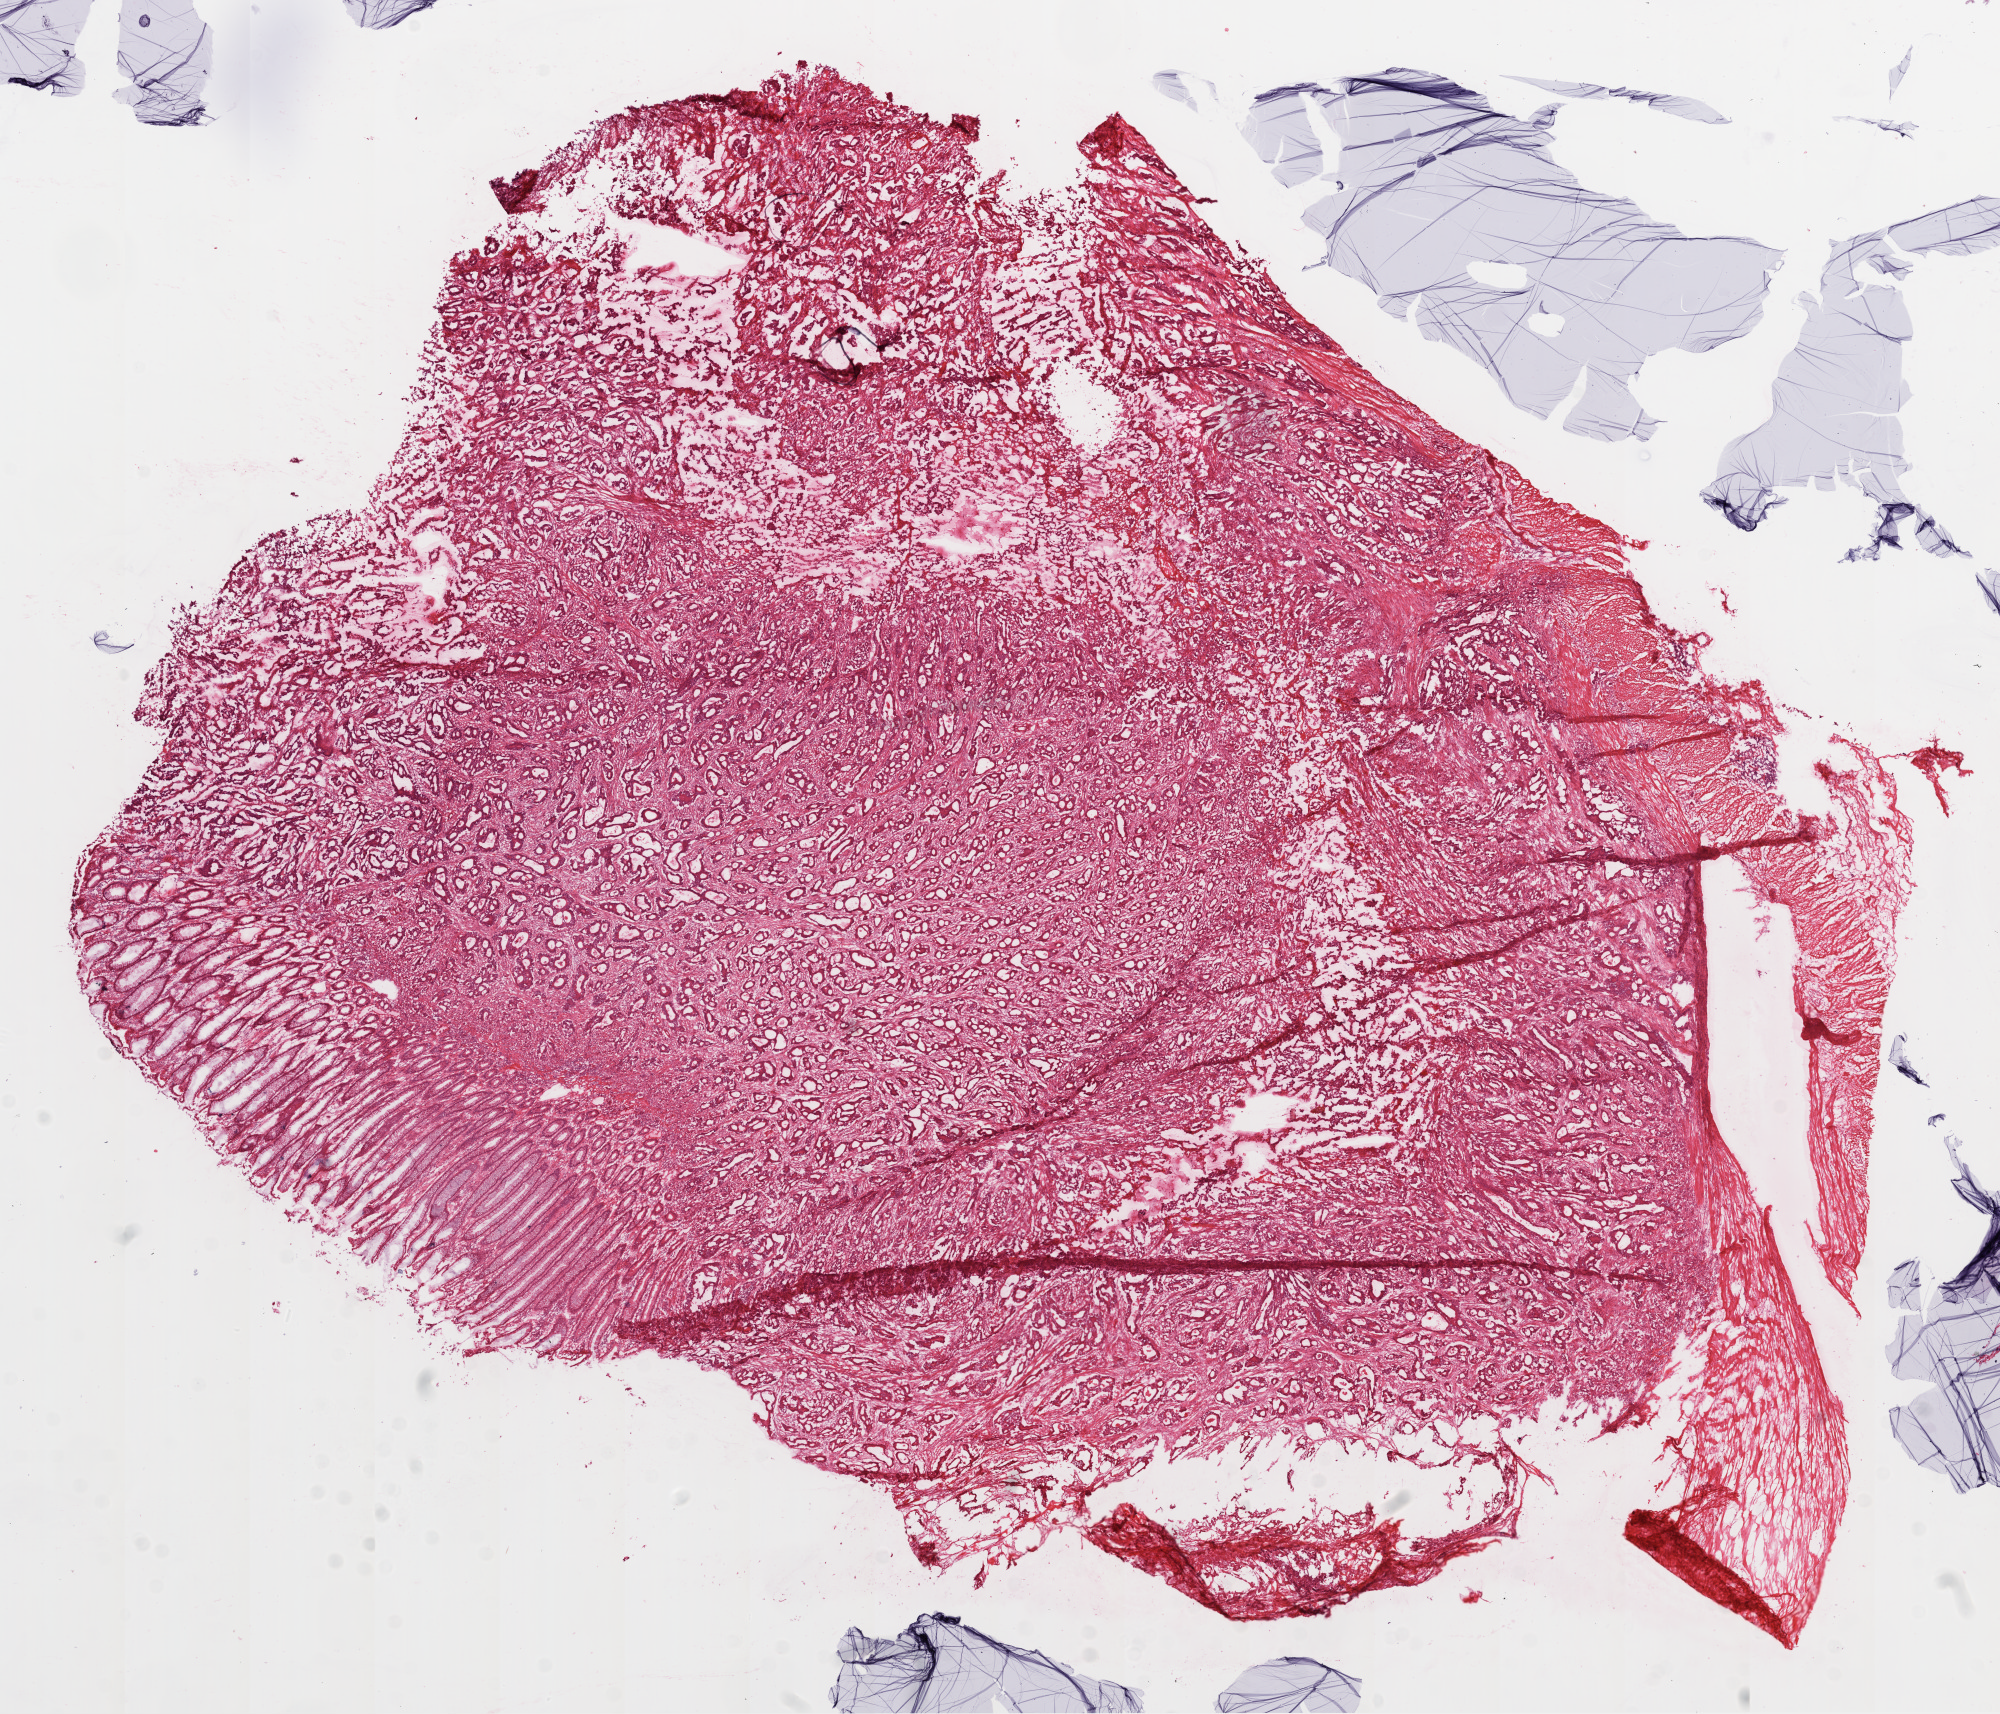
Hematoxylin and eosin (H&E) stained whole-slide image, low-resolution overview of the scanned area, about 16.0 x 13.8 mm (from a 20x scan); frozen section; sample: primary tumour, colon. Female patient; age at initial diagnosis 47 years. Pathologist review of this section (percent, as recorded): tumour cells 80%, tumour nuclei 85%, normal cells 15%, stromal cells 5%, necrosis 0%. Infiltration values recorded for this section: lymphocyte infiltration 2%.
AJCC pathologic stage: IIIB (6th edition). Diagnosis: Adenocarcinoma, NOS (sigmoid colon). Lymph nodes positive (case pathology): 3 of 14 examined. TNM: T3 N1 M0.